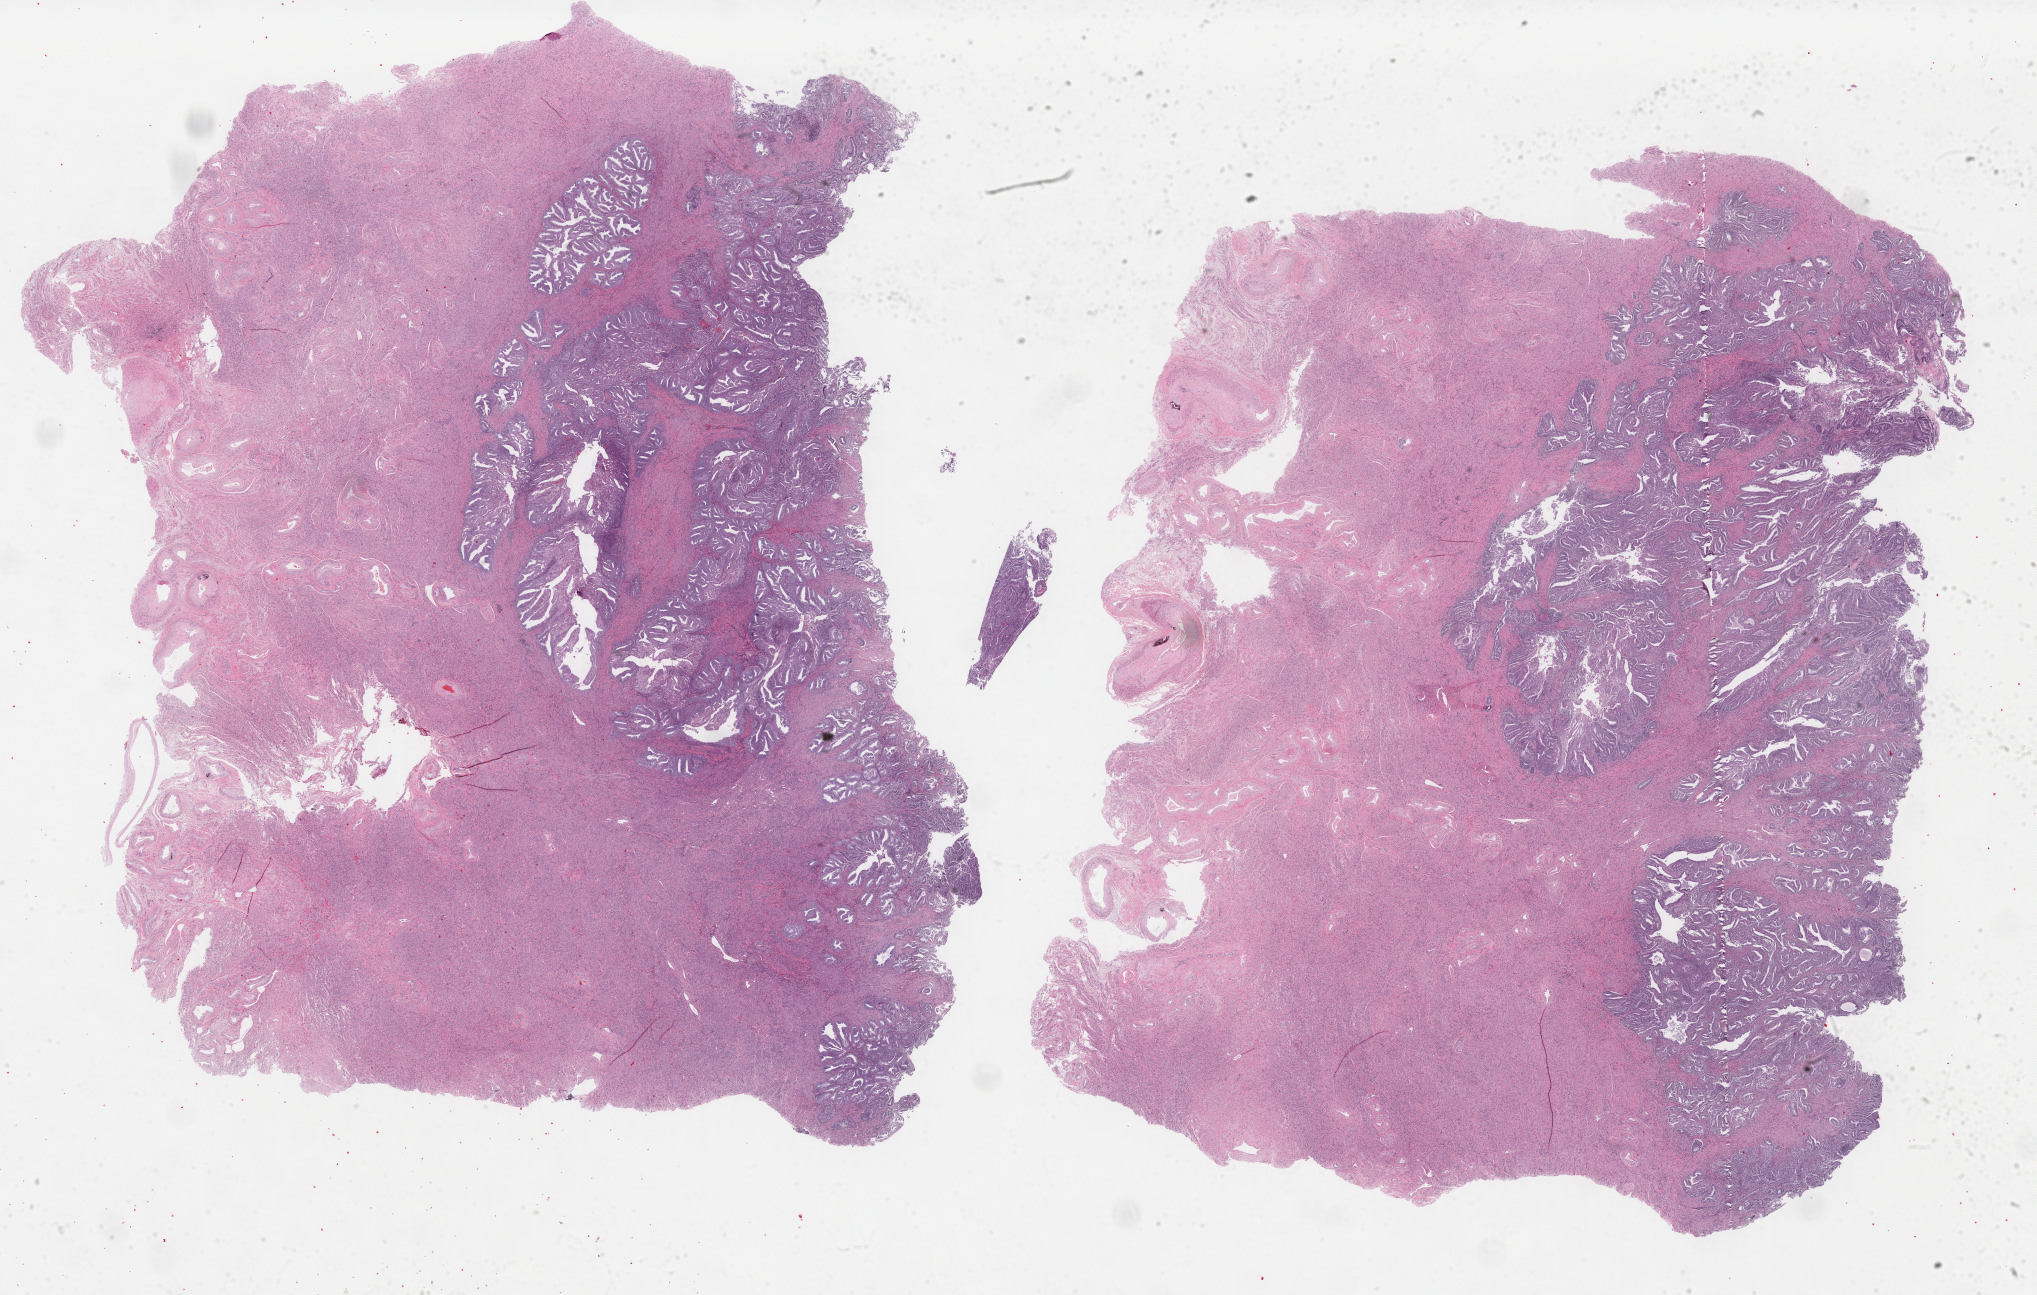
Whole-slide histology image, H&E-stained, whole scanned area (about 32.3 x 20.6 mm) shown as a low-resolution overview. Formalin-fixed paraffin-embedded (FFPE) diagnostic section. Primary tumour sample from the uterus. Patient: female, age at initial diagnosis 78 years.
Histologic diagnosis: Endometrioid adenocarcinoma, NOS (endometrium).